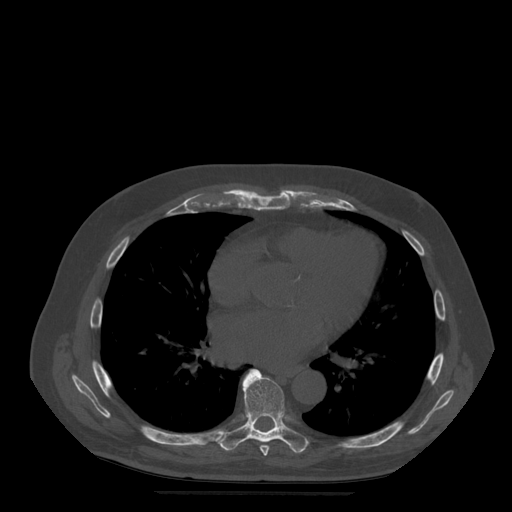
CT including the spine, one axial slice; slice 316 of 522 in the series (ordered by position); bone window (W 1800 / L 400 HU); 512 × 512 image matrix. Patient age 72 years. Case-level facts recorded for this patient, not image findings: primary cancer: prostate.
Outlined on this slice (semi-automatically segmented with operator editing):
- T7 vertebra: box from (x=260, y=445) to (x=270, y=456) px
- T8 vertebra: (x=218, y=369)–(x=309, y=454)